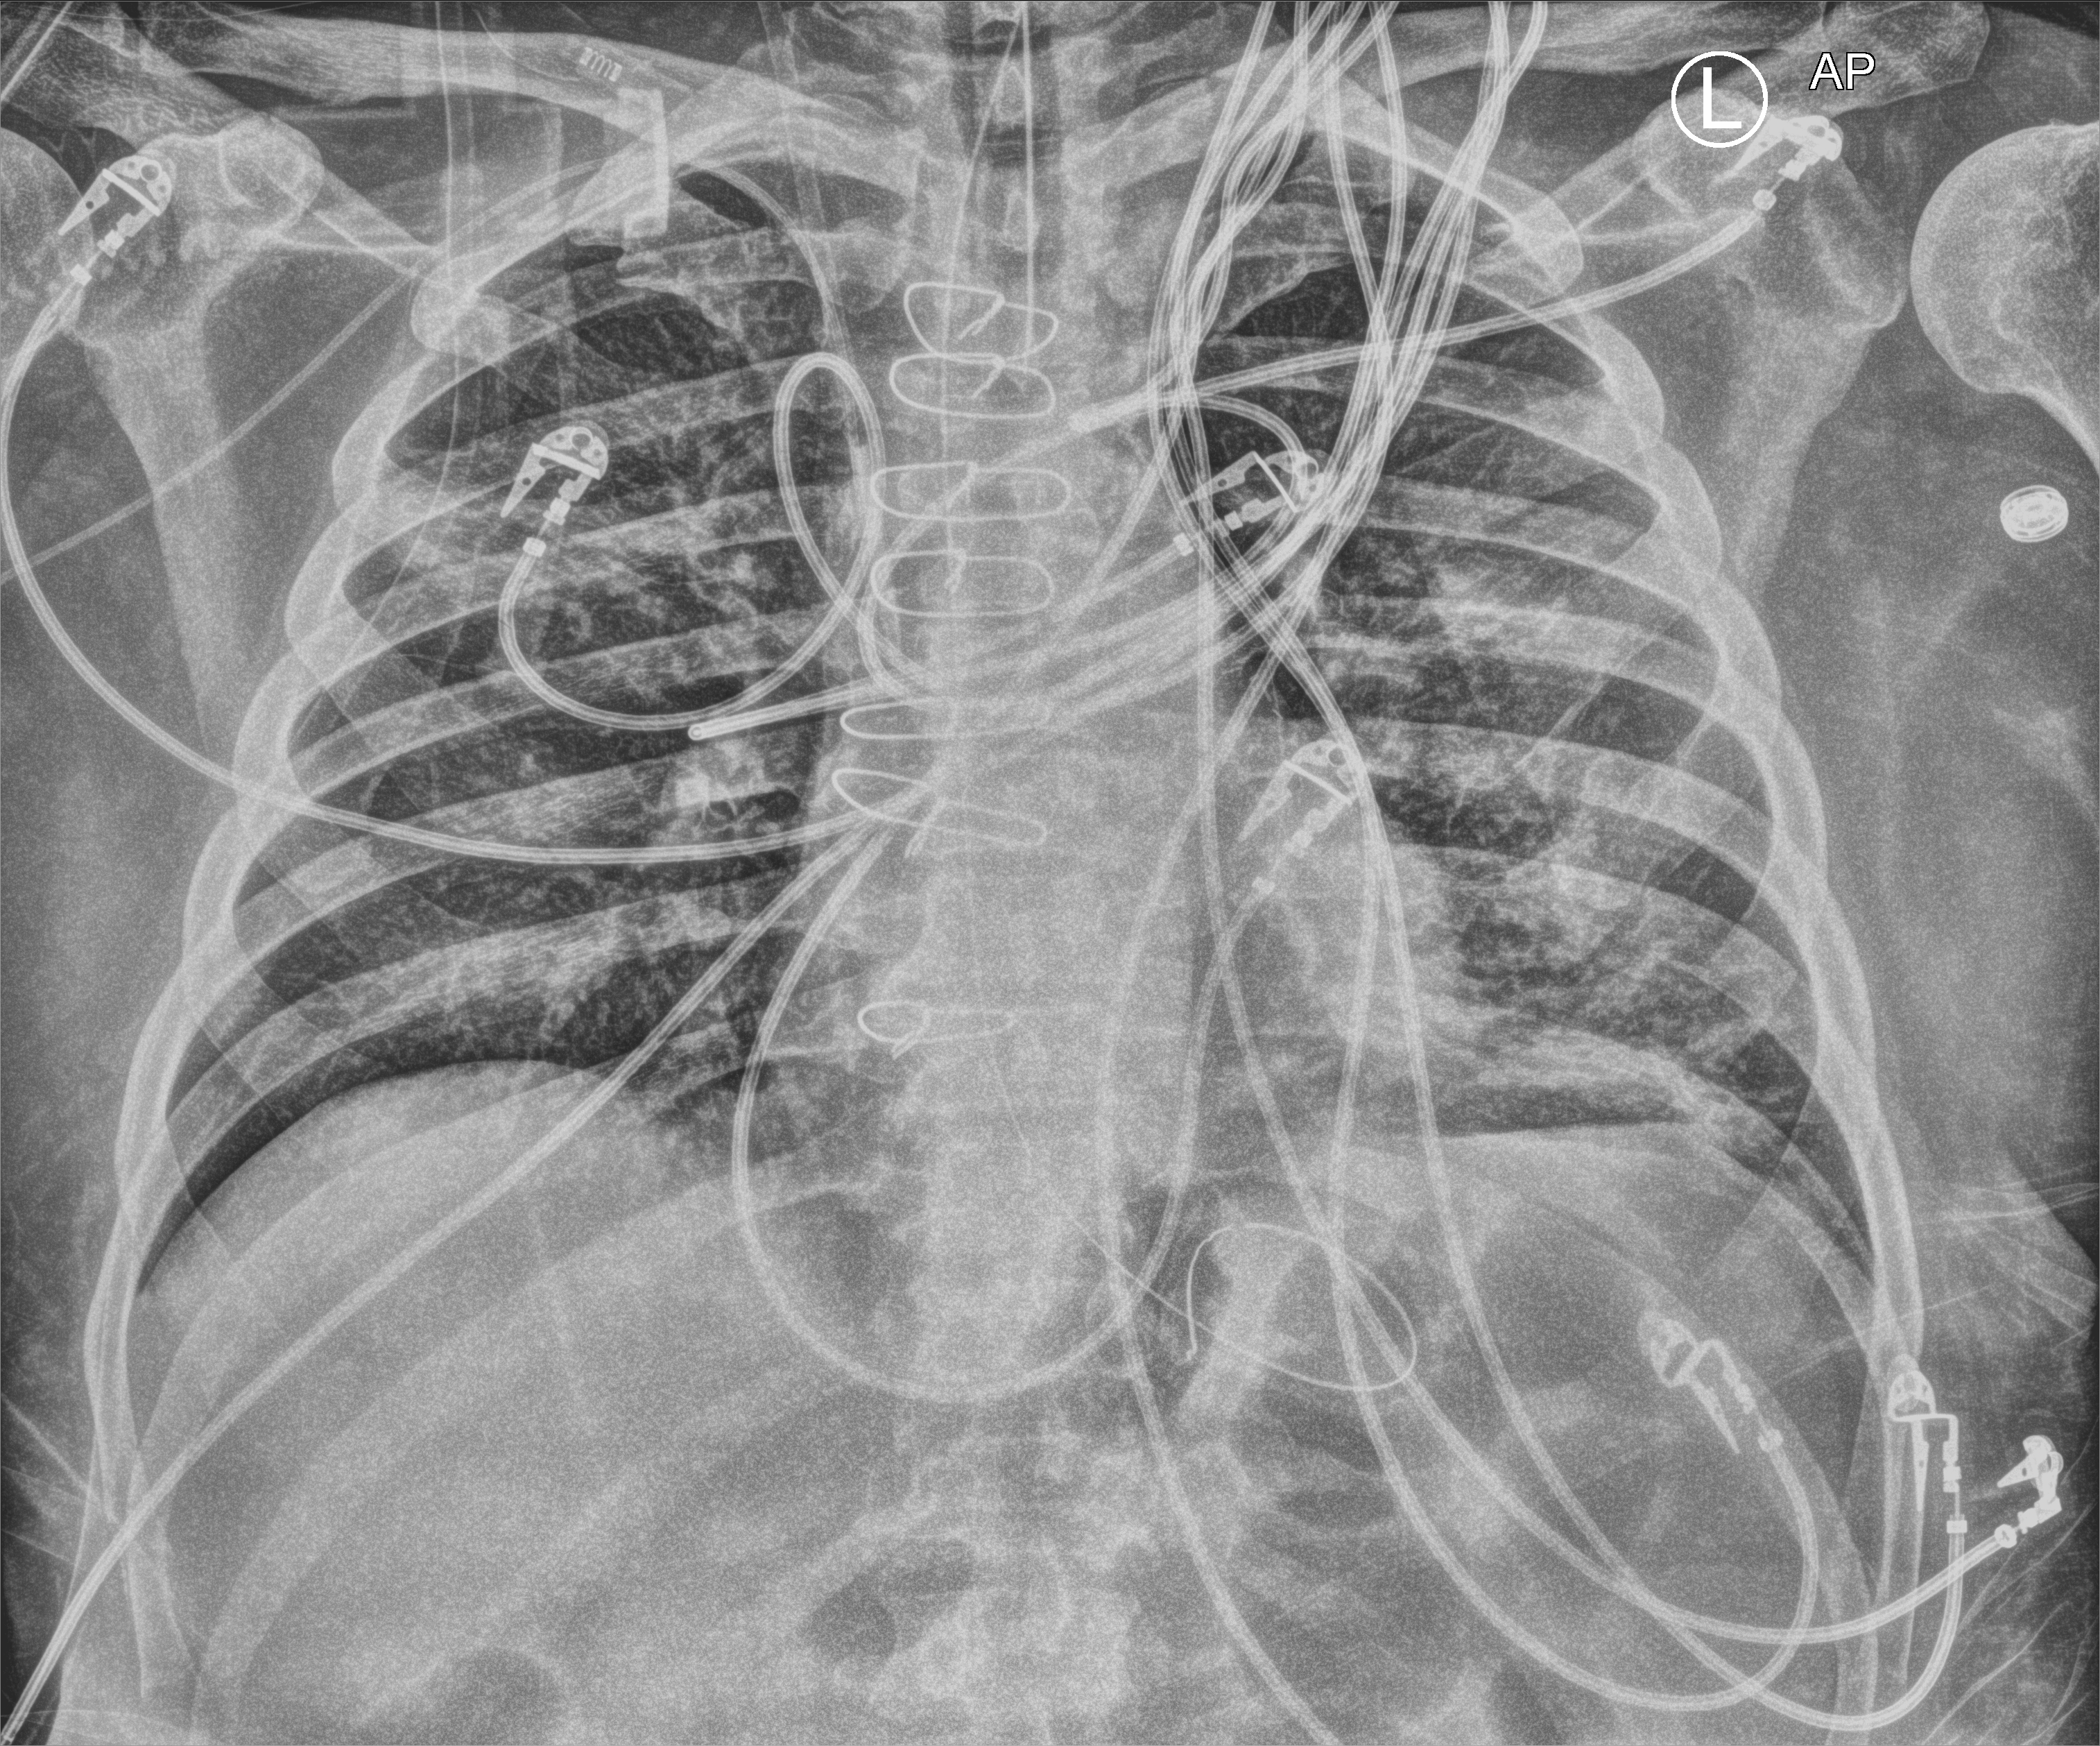
Portable chest radiograph. Patient hospitalised with COVID-19; male, aged 60–74 years.
Hospital-stay facts (about this admission, not read from this image; timing relative to this image not recorded): mechanically ventilated during this hospital stay: yes; smoking status (admission record): former; length of hospital stay: 44 days.